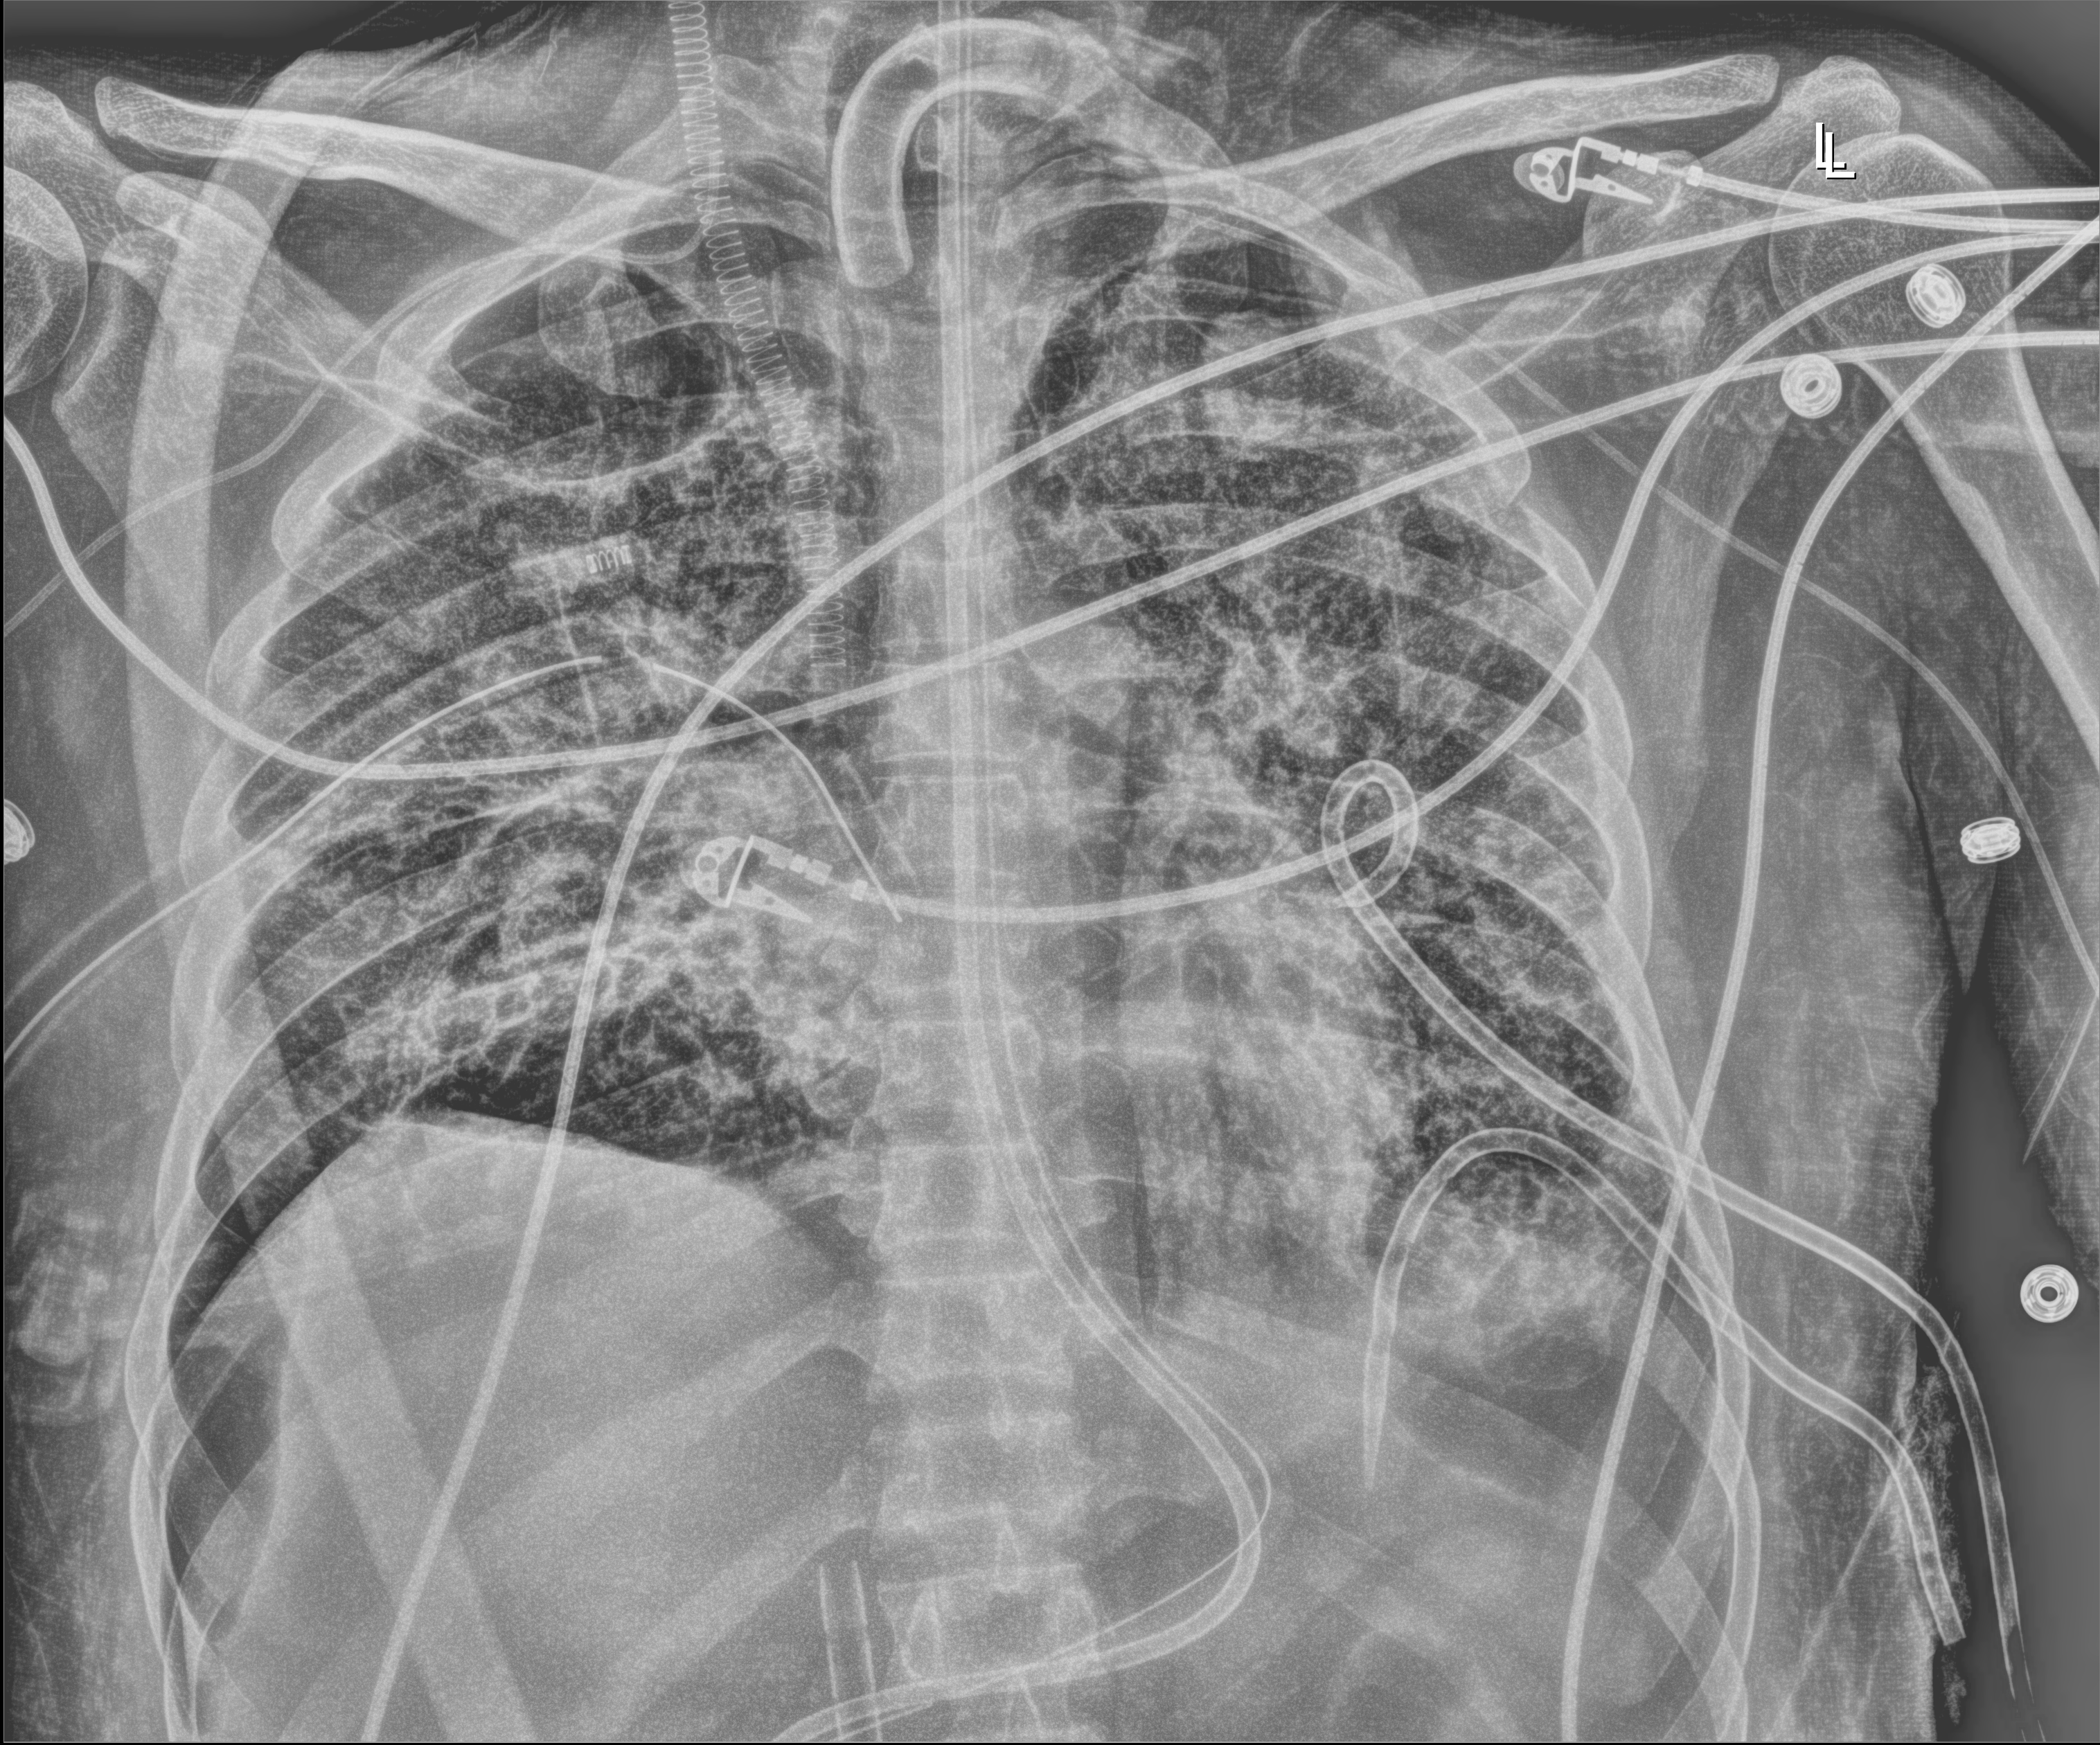
Portable chest radiograph; anteroposterior (AP) projection. Patient hospitalised with COVID-19, aged 18–59 years.
From the hospital-stay record, not from the radiograph (when in the stay this image was taken is not recorded):
- hypertension (admission record): no